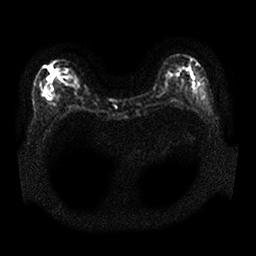
Breast MRI, one axial slice; position 10 of 25 along the scan axis; diffusion-weighted series; image 2 of 4 stored at this slice position (different b-values; order by instance number); 1.5 T; 4 mm slice thickness; 256 × 256 image matrix. Female patient.
Structures marked on this image (manually delineated by an expert):
- tumour on diffusion-weighted imaging: bounding box (x1, y1, x2, y2) in pixels: (46, 69, 53, 84)